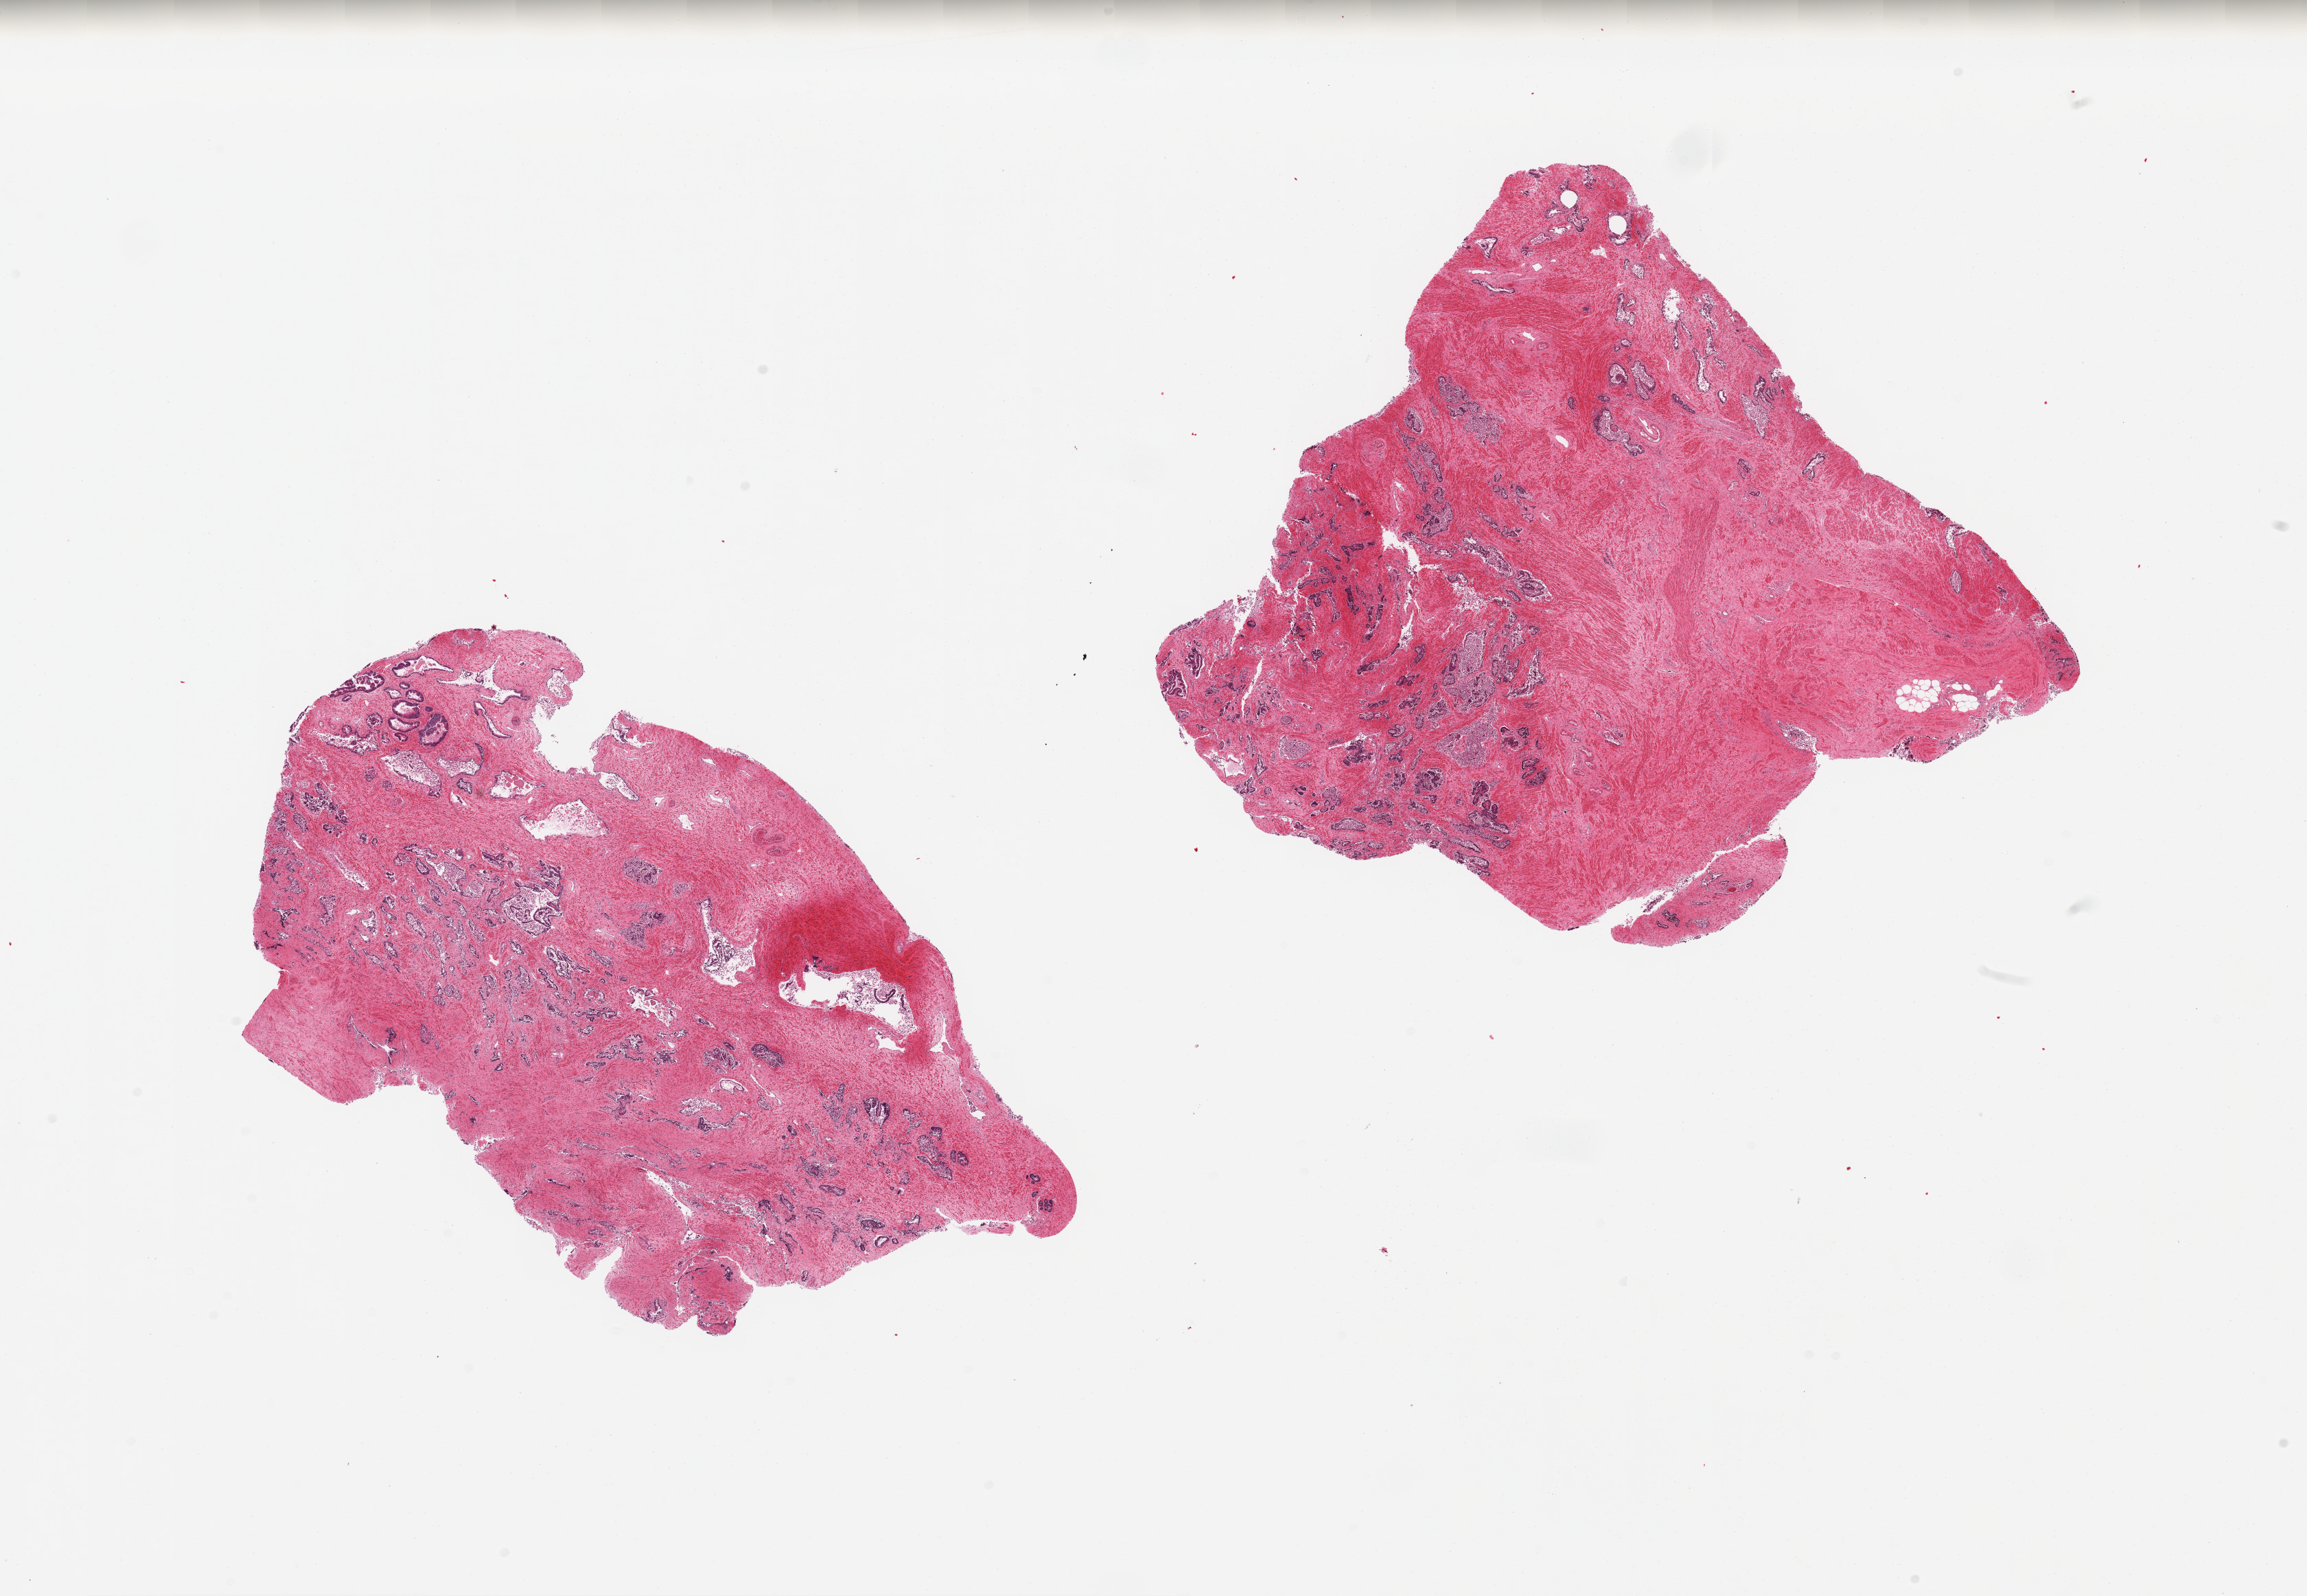
Whole-slide image, haematoxylin and eosin stain, whole scanned area (about 26.6 x 18.4 mm, slide scanned at 20x) shown as a low-resolution overview, PAXgene-fixed paraffin-embedded (PFPE) section, sampled site (target tissue): prostate, tissue donor sample. Male donor.
- review note (as recorded): 2 pieces, glandular component moderate-marked autolysis (2-3)